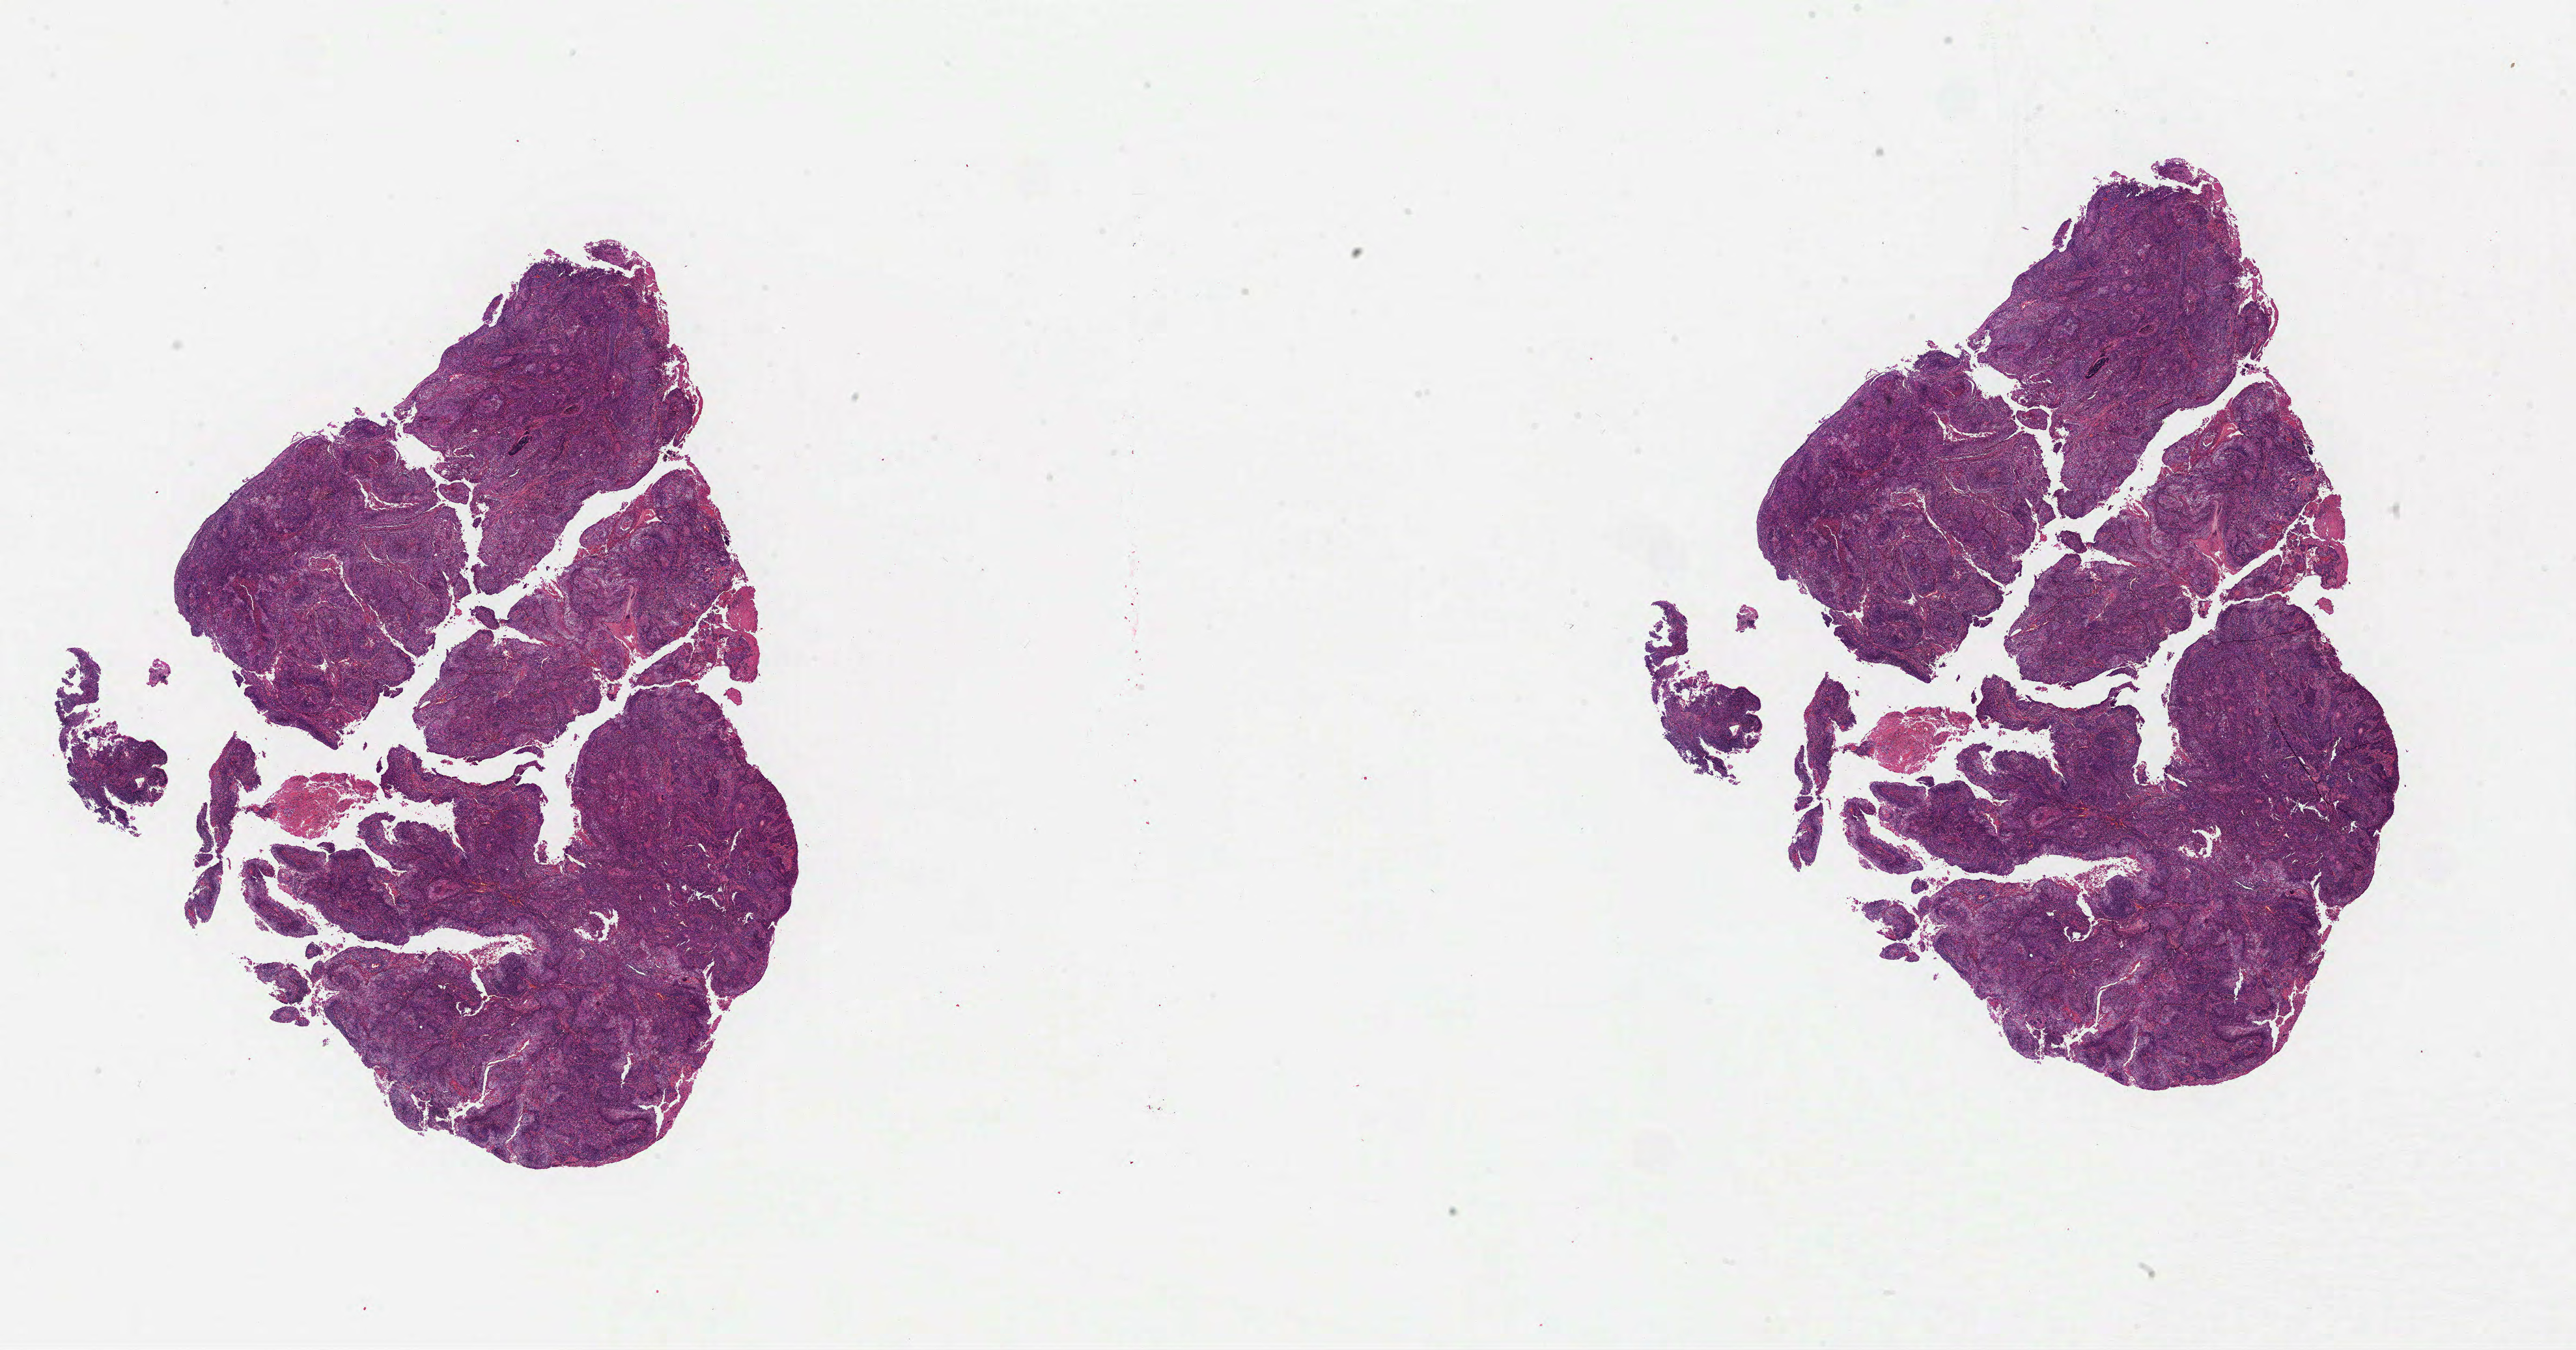
Whole-slide histology image, H&E-stained — a low-resolution overview of the entire scanned area, about 31.9 x 16.7 mm (slide scanned at 40x). FFPE section. Primary tumour sample from the lung. Male, age 65 years at initial diagnosis.
Diagnosis: Squamous cell carcinoma, NOS (upper lobe, lung).